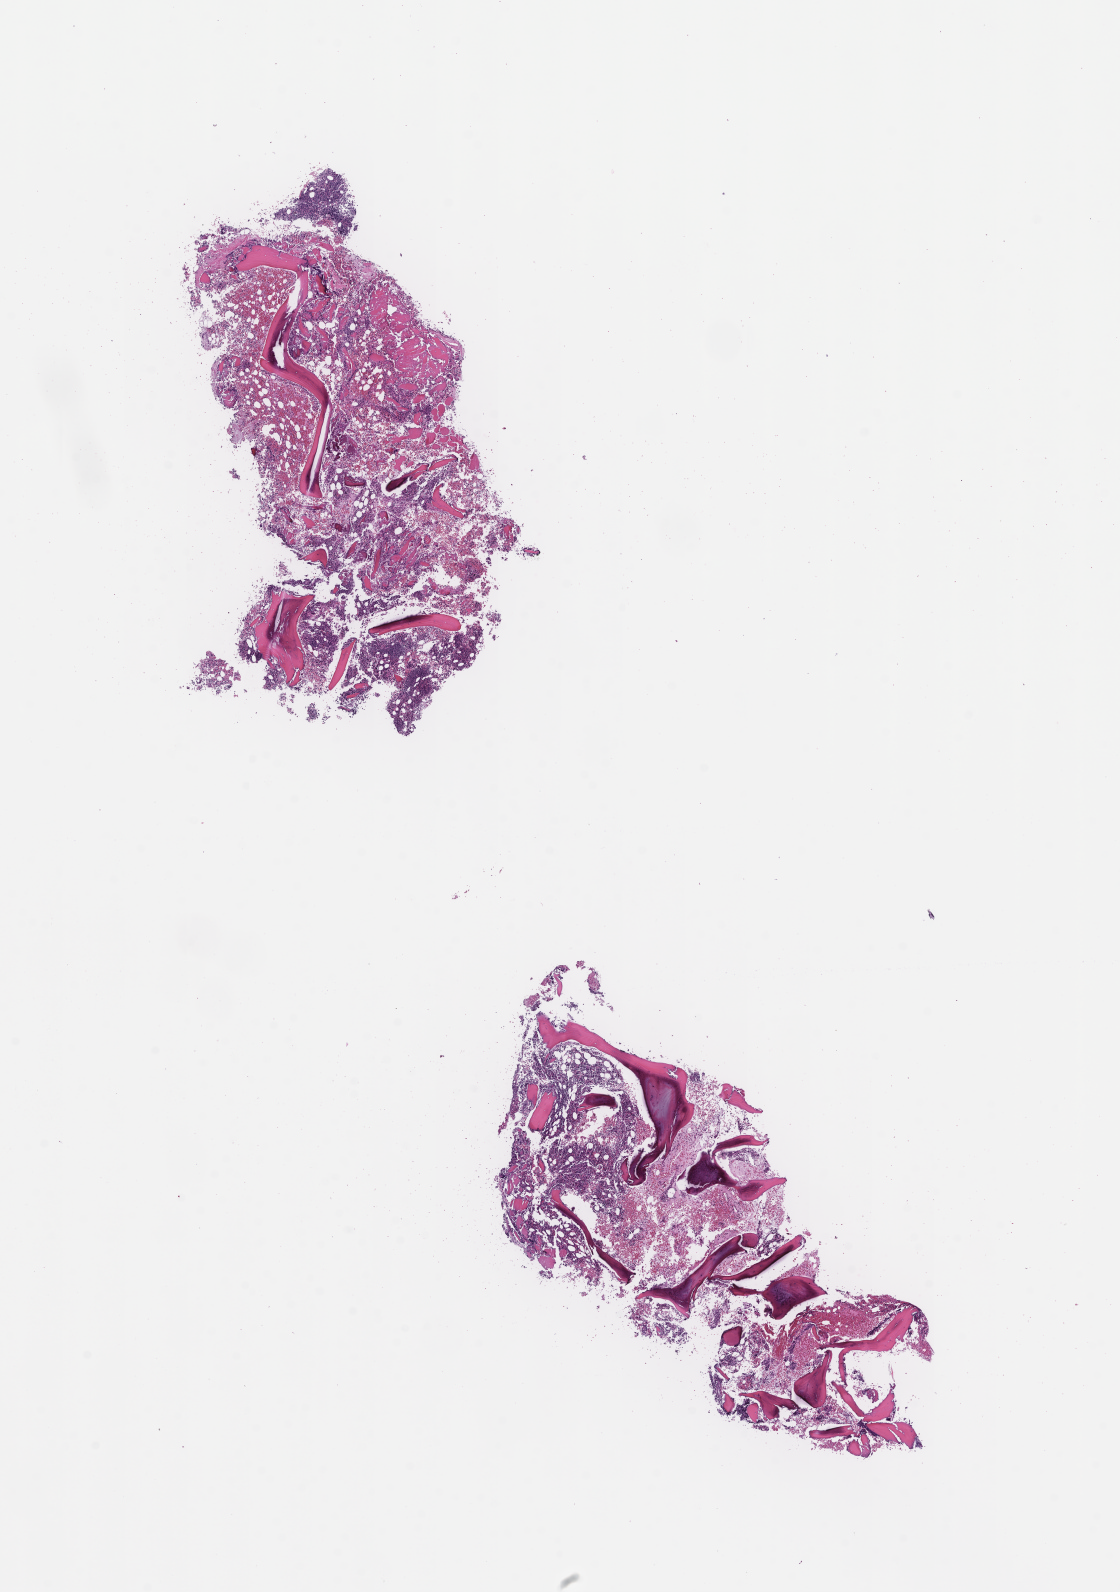
Digitized haematoxylin and eosin-stained section — low-resolution overview of the scanned area, about 9.0 x 12.9 mm; FFPE section; tissue site: bone marrow. Patient: male.
- this section: primary tumour tissue
- diagnosis: Plasma Cell Myeloma